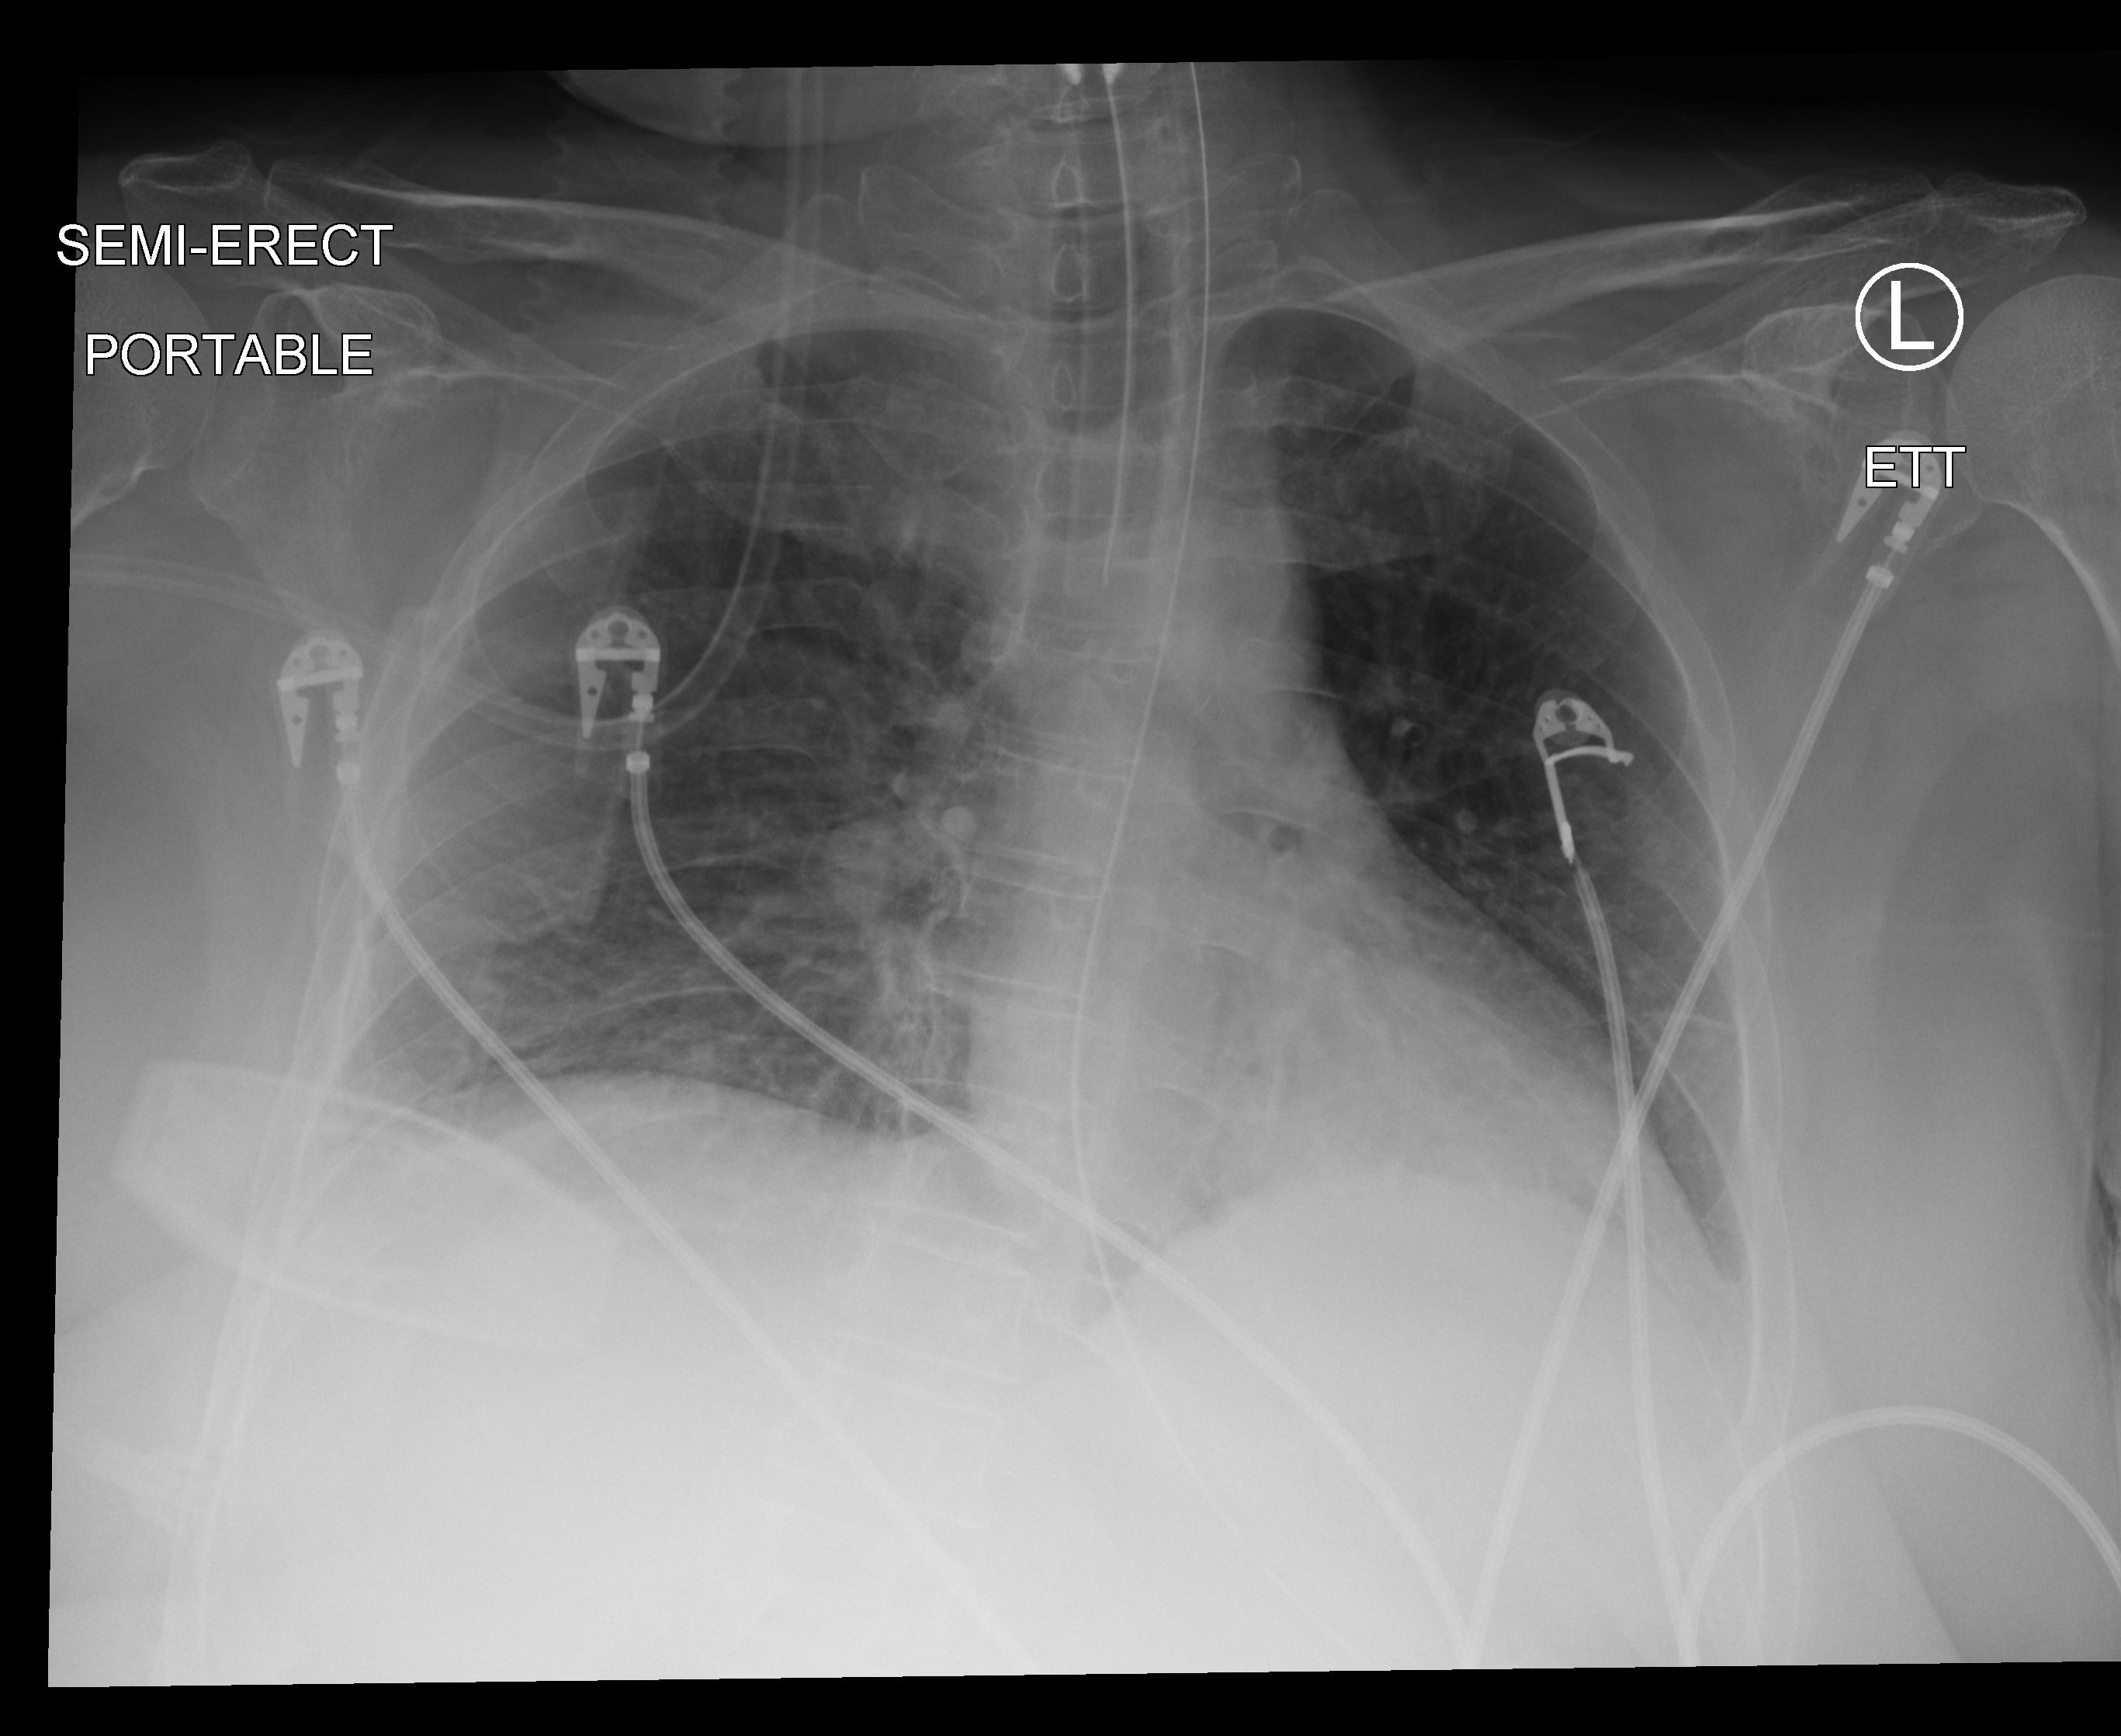
Bedside chest radiograph (computed radiography), anteroposterior (AP) projection. Female patient hospitalised with COVID-19, age 18–59 years.
Hospital-stay facts (about this admission, not read from this image; timing relative to this image not recorded): mechanically ventilated during this hospital stay: no; admitted to intensive care during this hospital stay: yes.